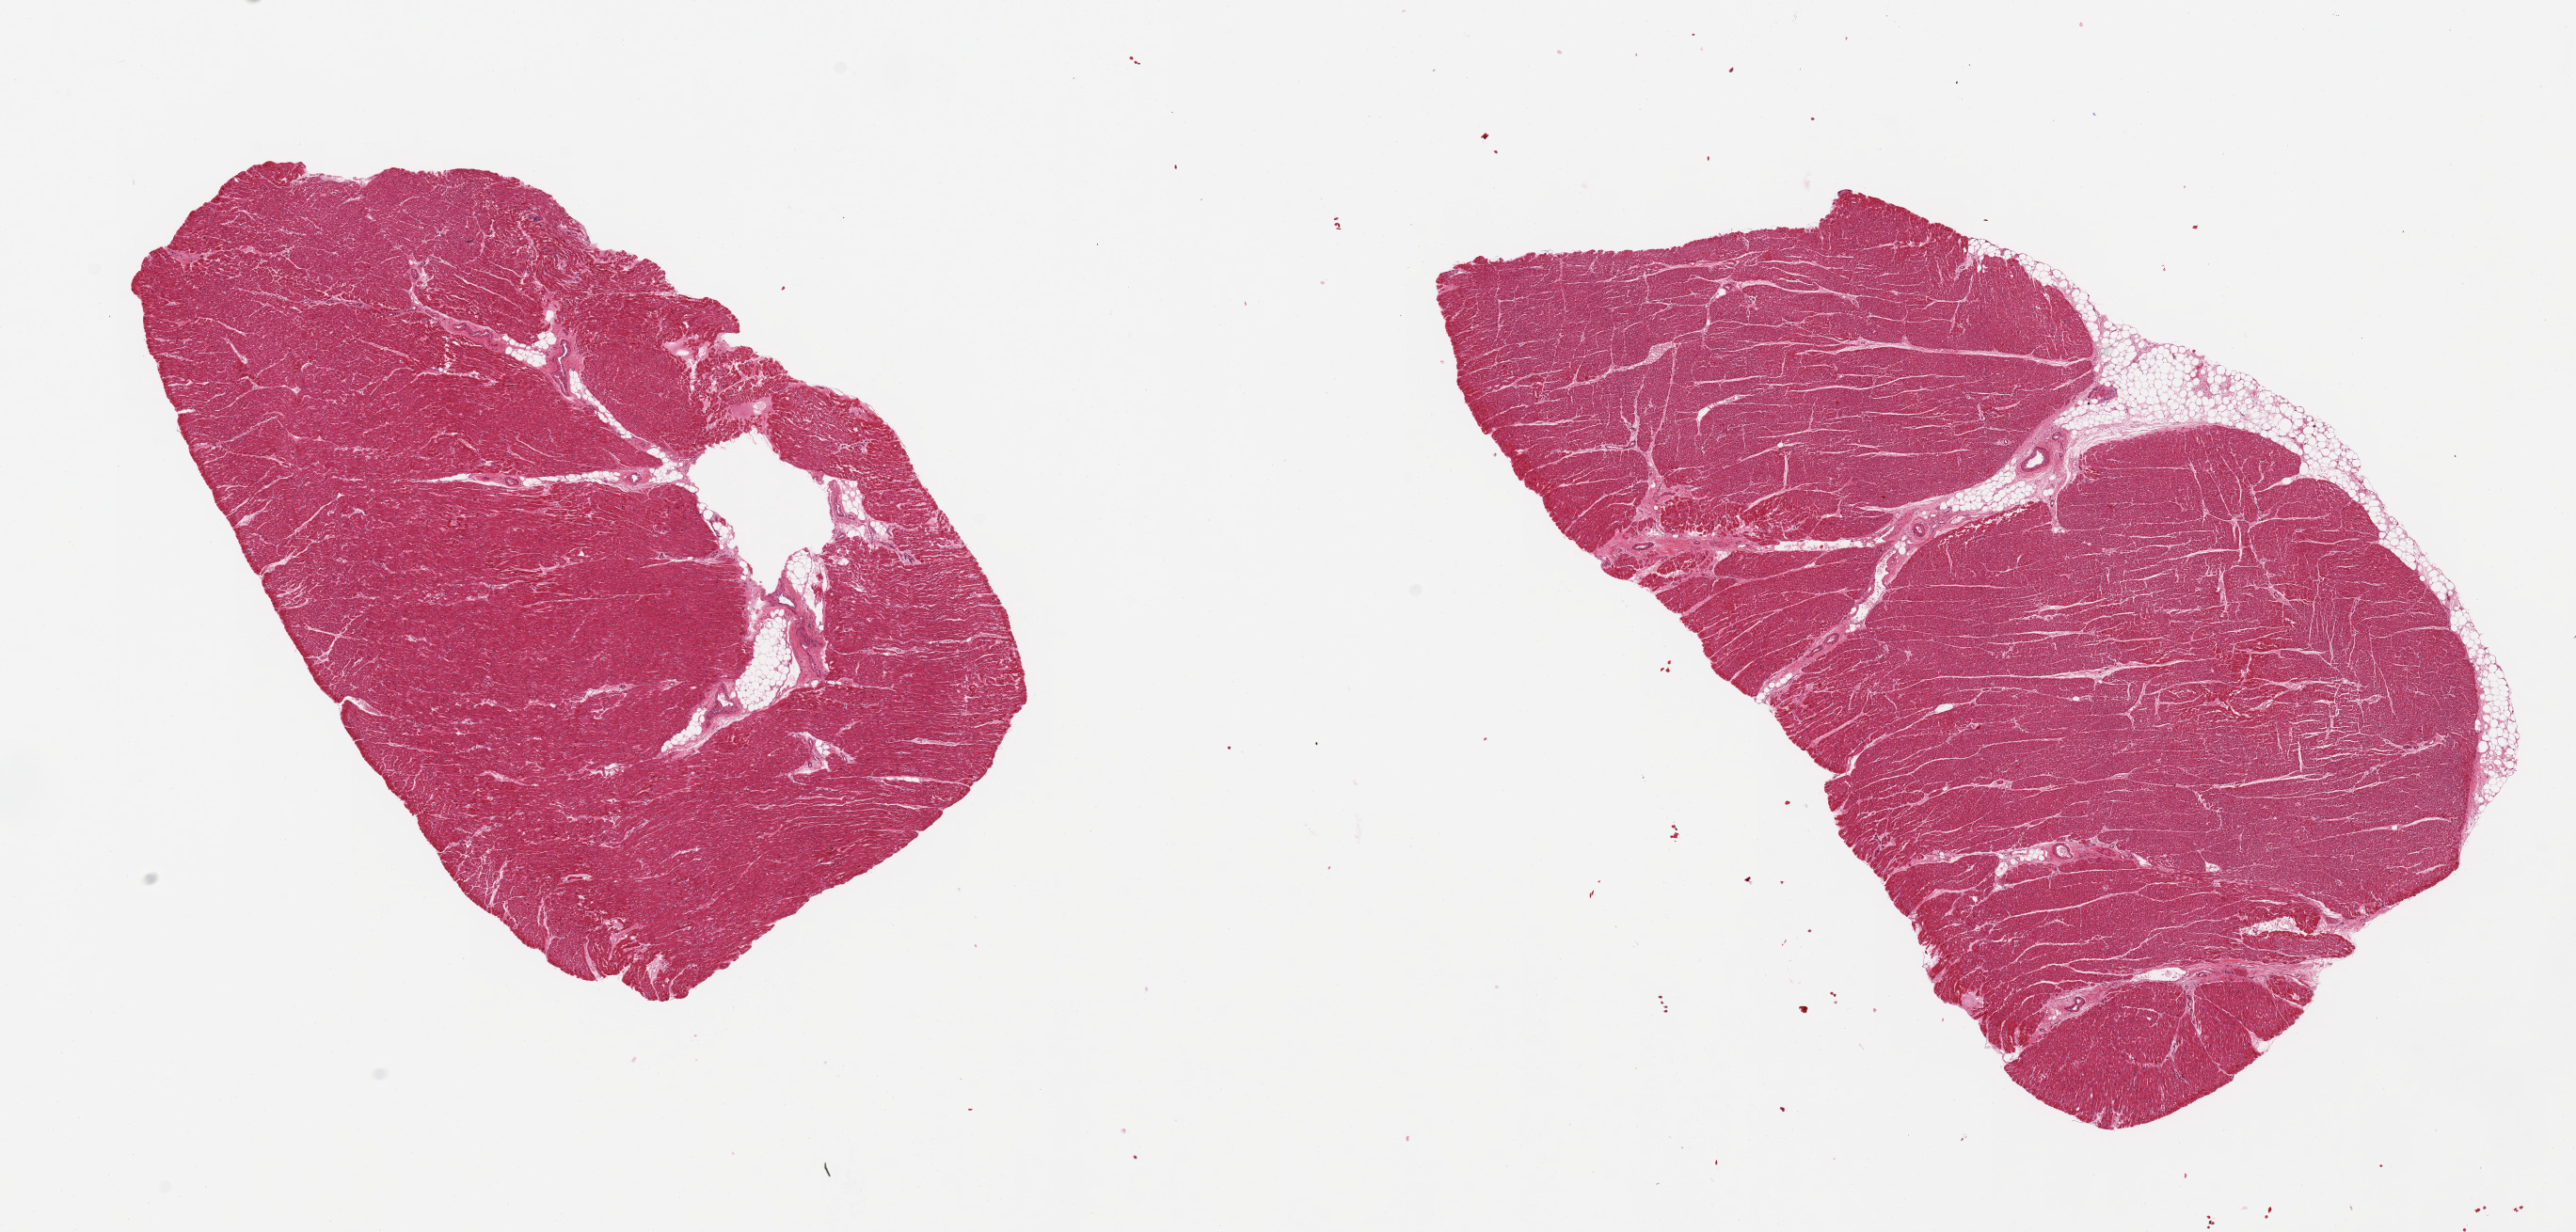
Whole-slide image, haematoxylin and eosin stain, whole scanned area (about 21.7 x 10.4 mm) shown as a low-resolution overview, PAXgene-fixed, paraffin-embedded tissue, sampled site (target tissue): heart, tissue donor sample. Female donor.
• reviewer comment on this tissue sample: 2 pieces, minimal ischemic changes